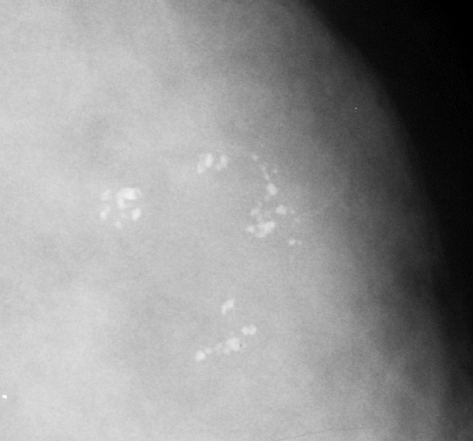
Cropped region of a digitized screen-film mammogram centred on a radiologist-marked abnormality; left breast; CC view.
- Calcifications, morphology pleomorphic, distribution clustered; BI-RADS assessment category 4; subtlety rating 5 on a 1 (subtle) to 5 (obvious) scale; pathology (as recorded): benign.